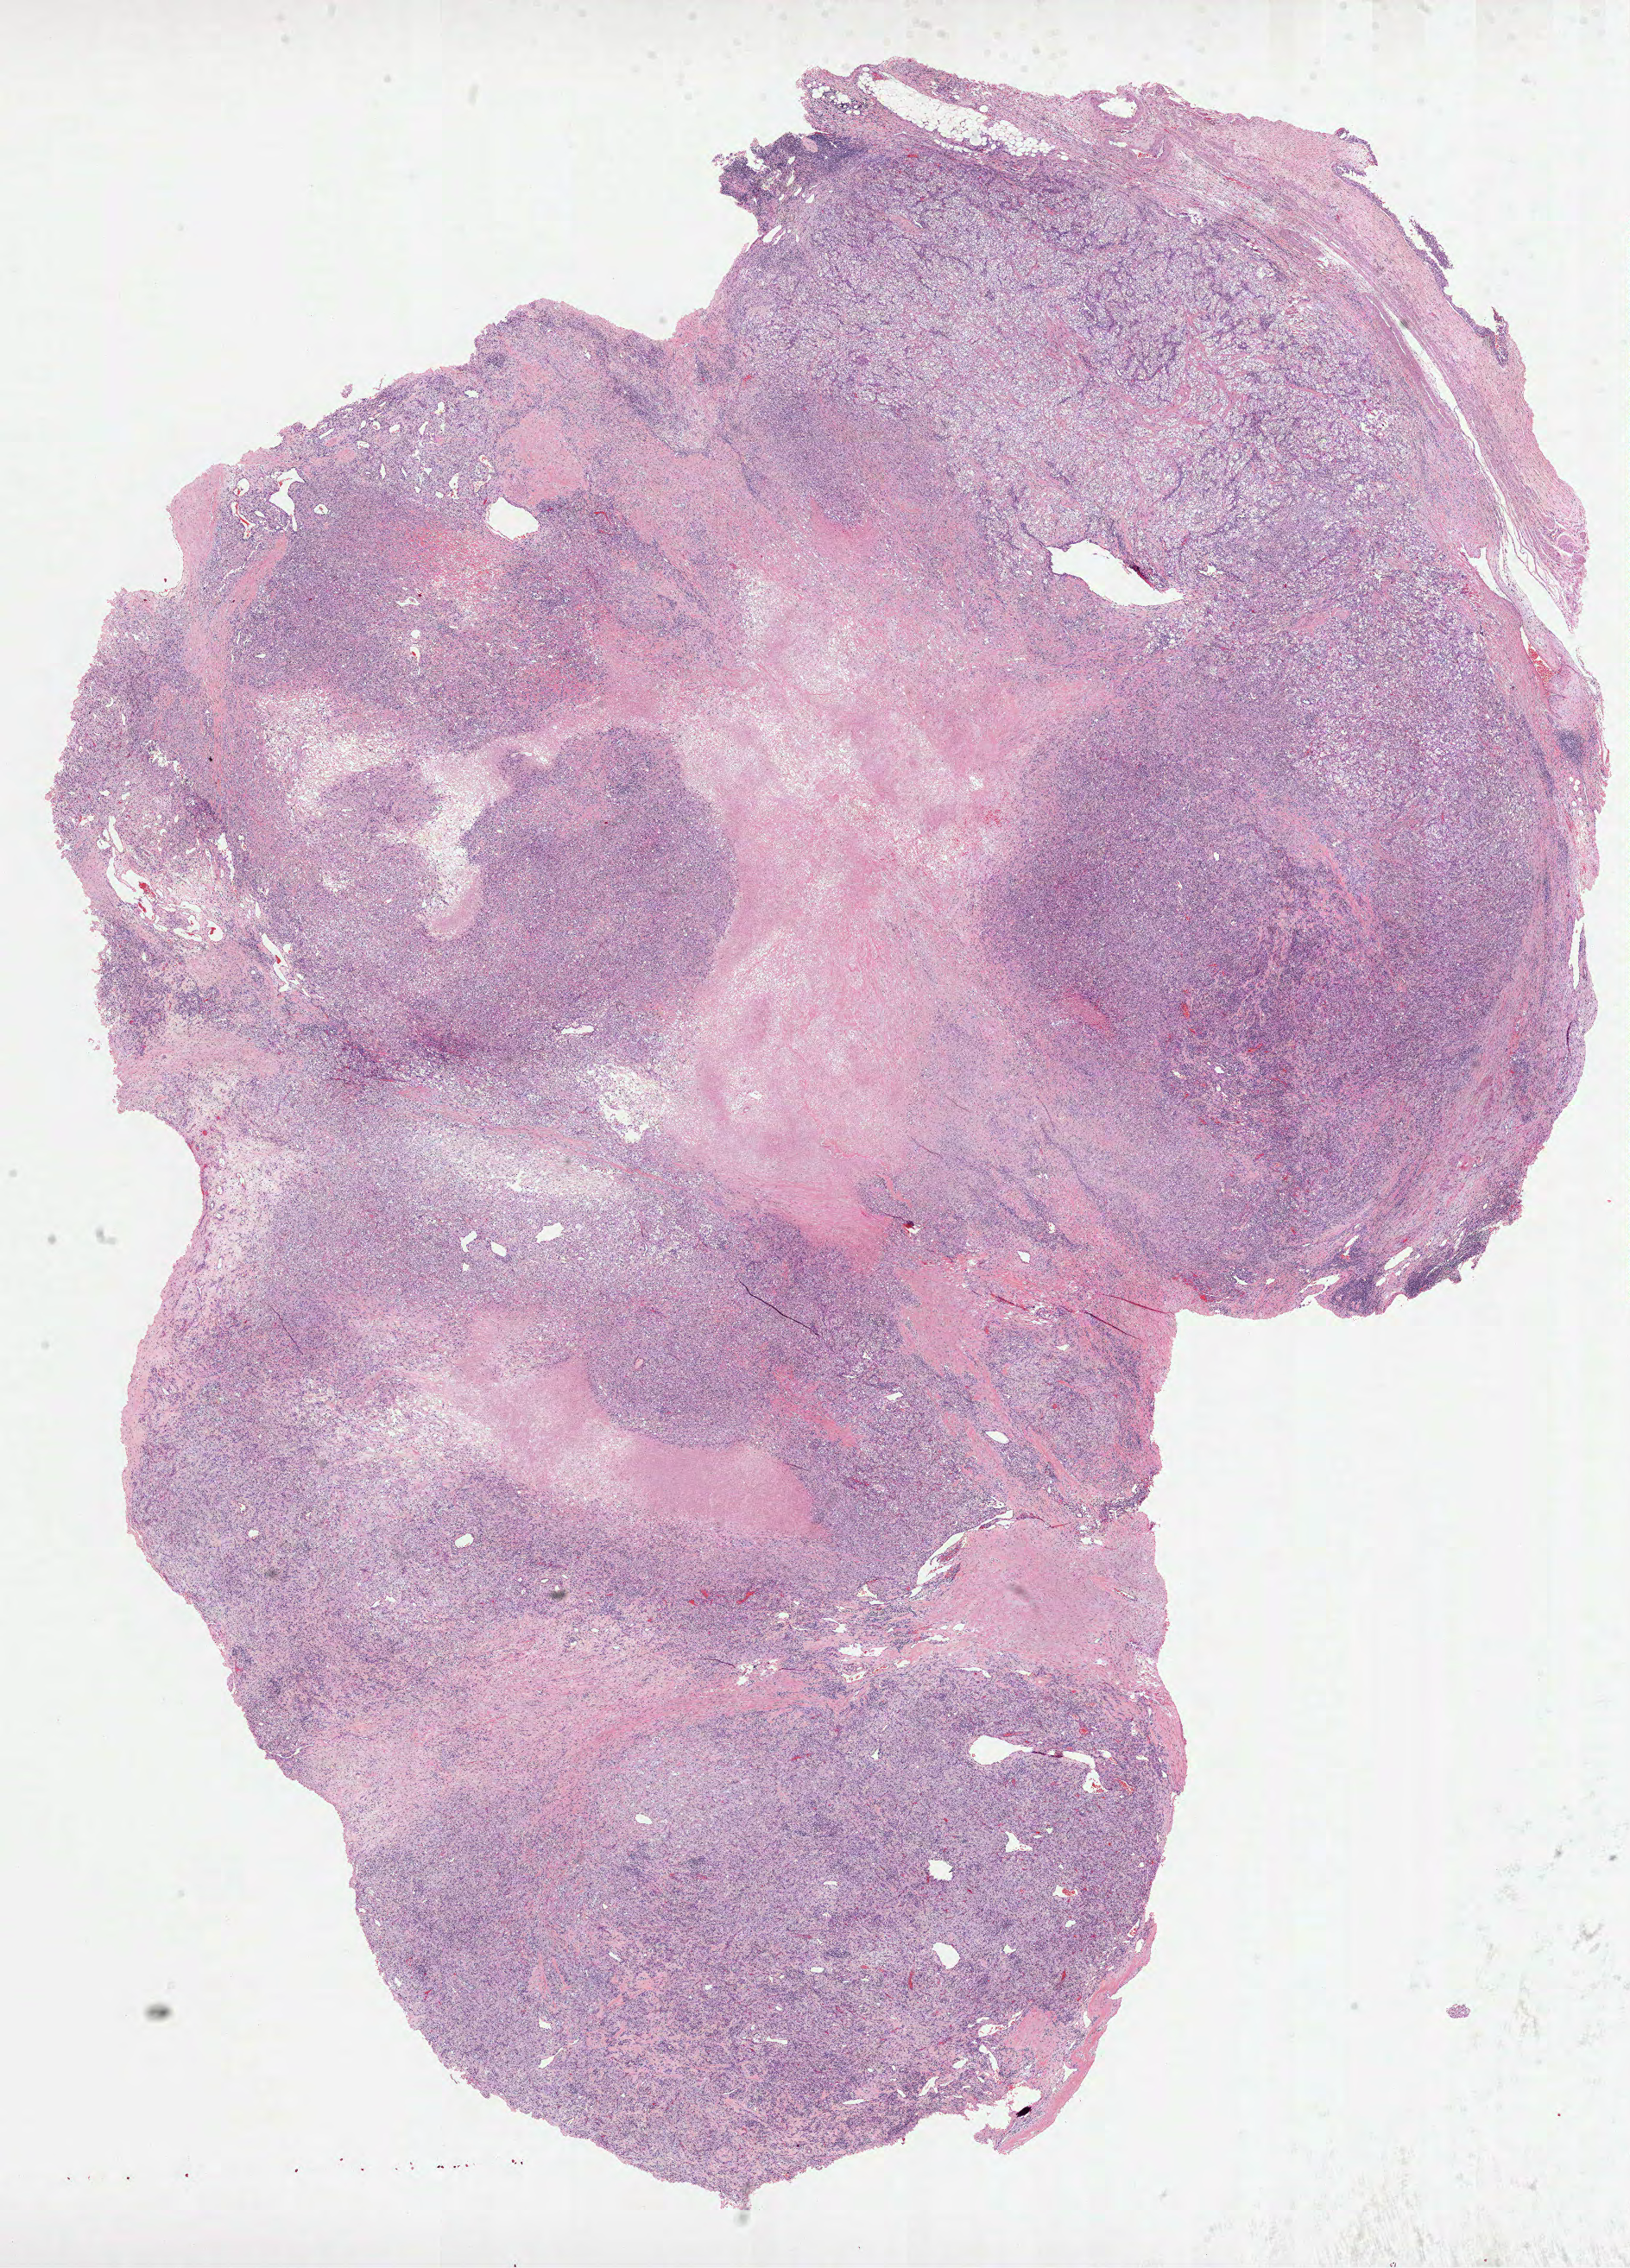
Whole-slide histology image, H&E-stained — whole scanned area (about 15.2 x 21.2 mm) shown as a low-resolution overview, formalin-fixed paraffin-embedded (FFPE) diagnostic section, kidney, primary tumour sample. Female, age 53 years at initial diagnosis.
Histologic diagnosis: Clear cell adenocarcinoma, NOS.